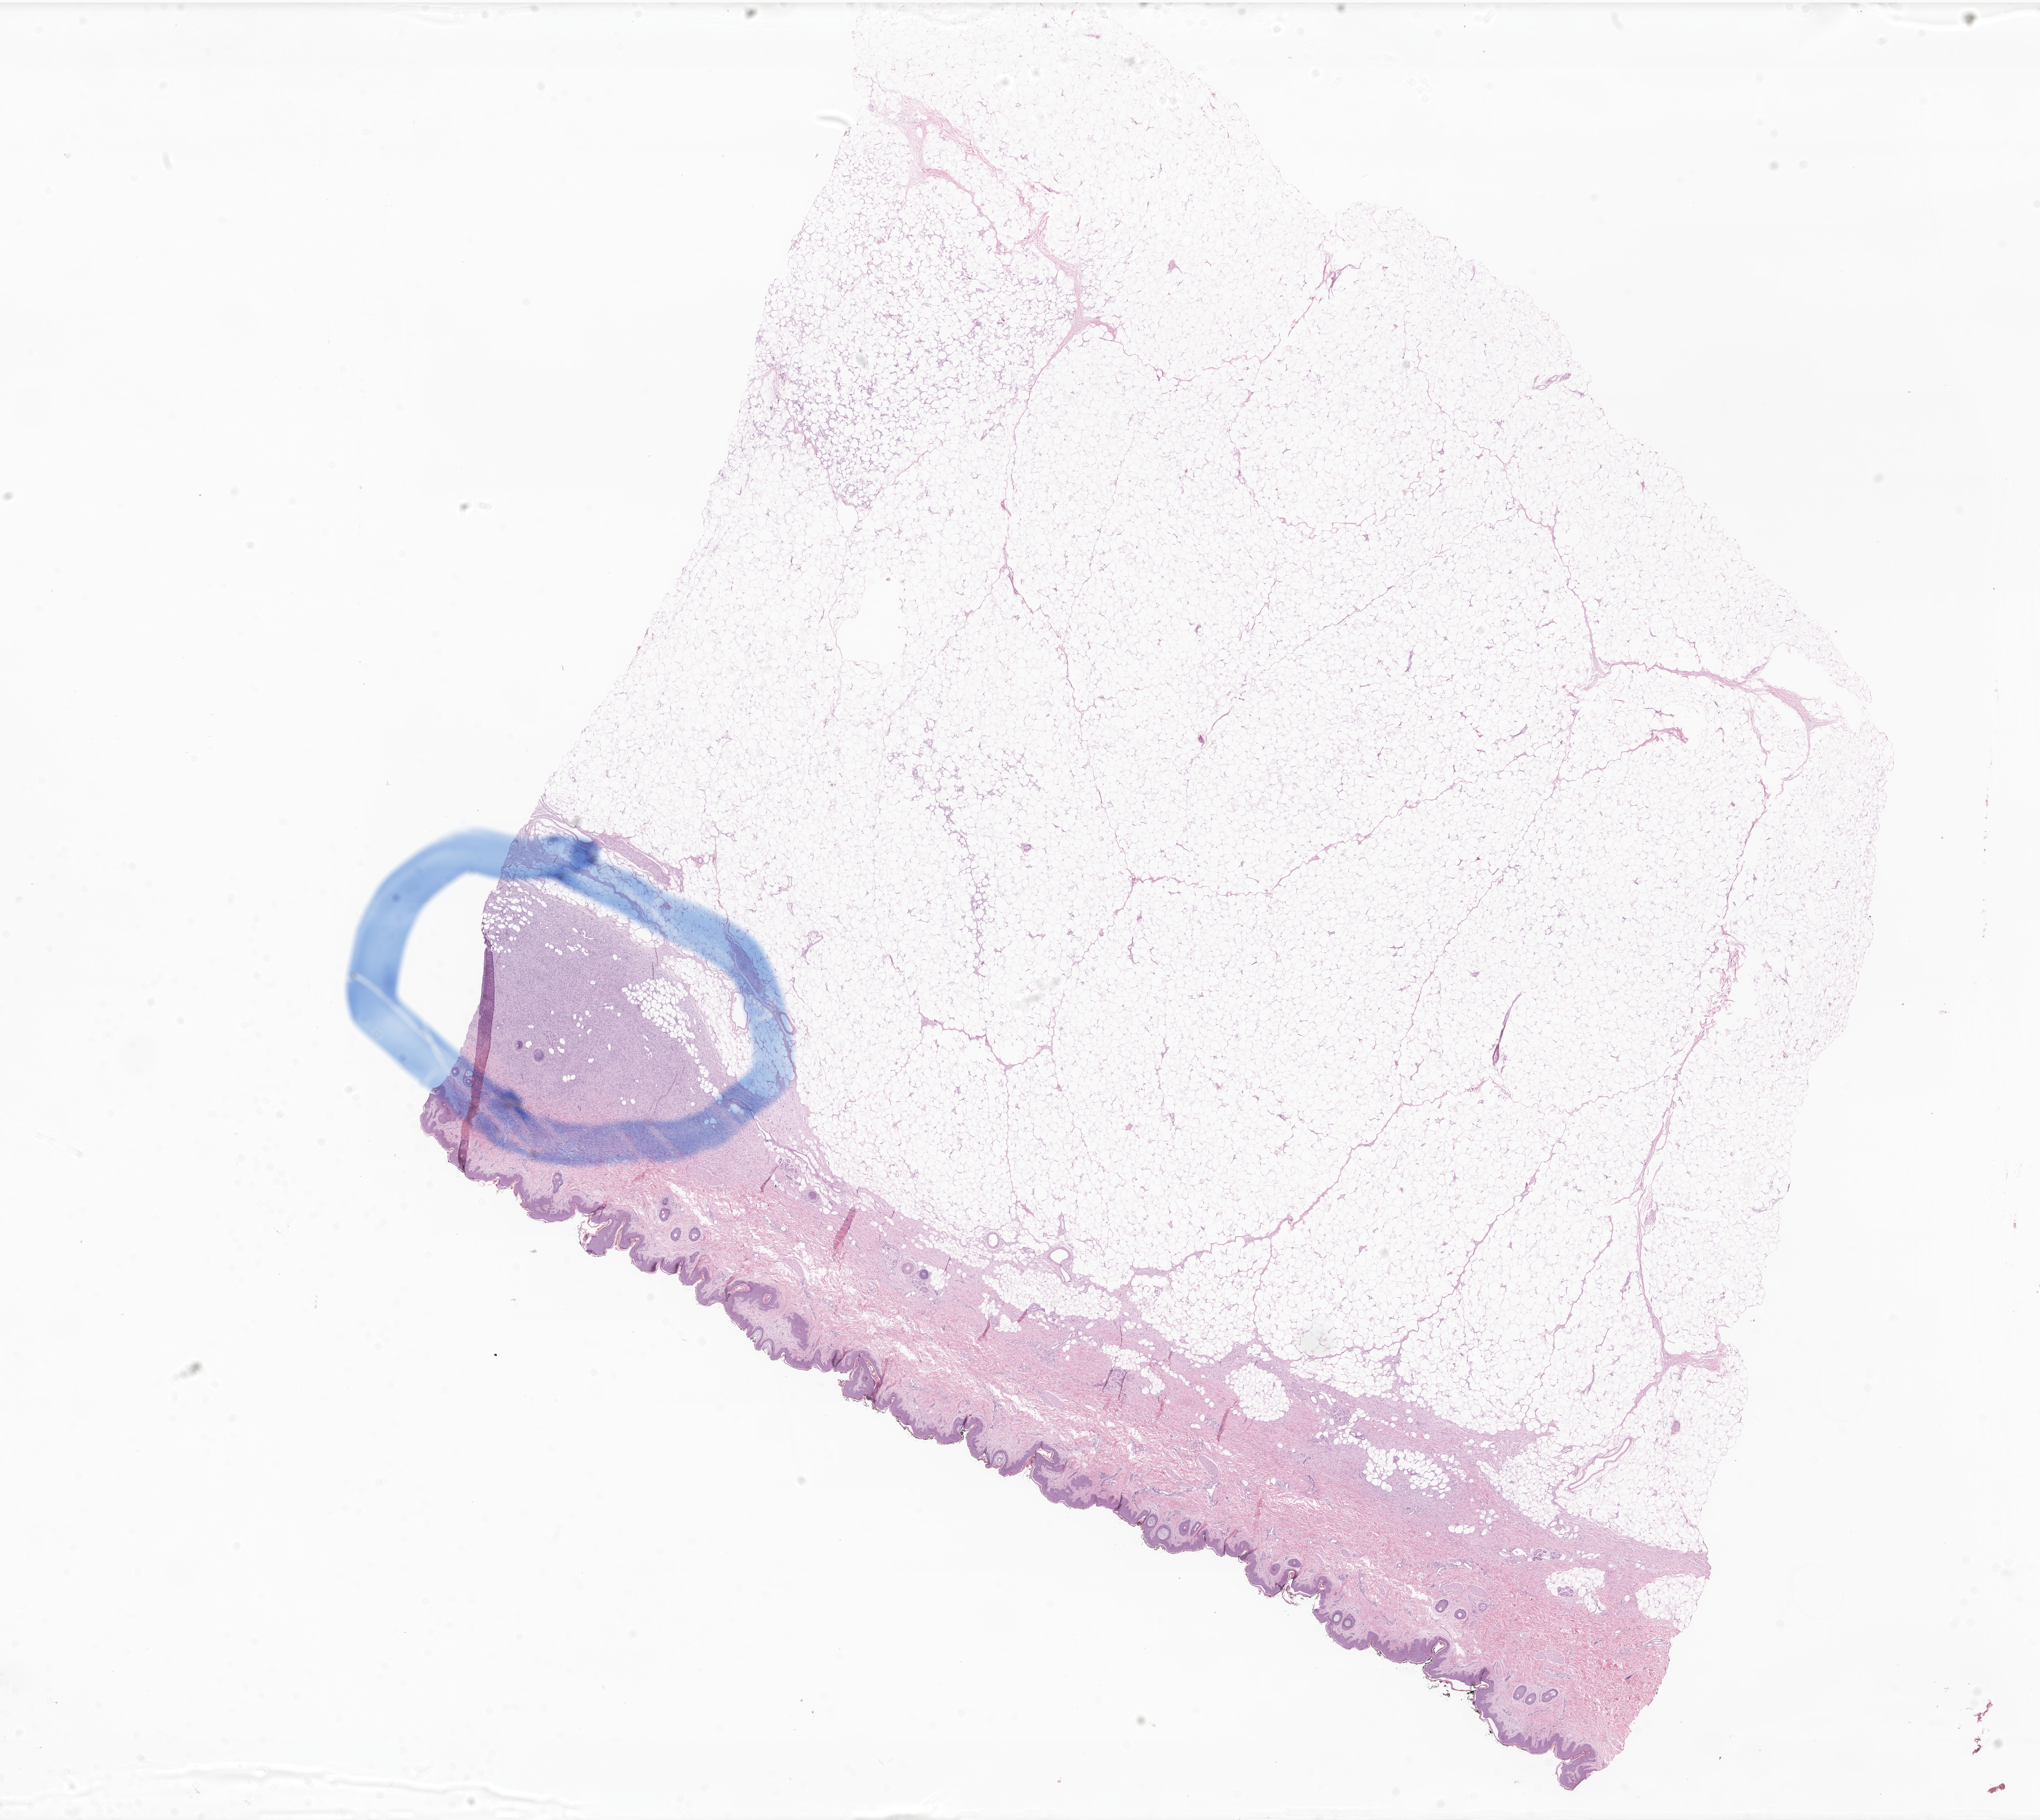
Digitized hematoxylin and eosin (H&E)-stained section of tumor tissue from the soft tissue of pelvis — a low-resolution overview of the entire scanned area, about 26.0 x 23.2 mm; formalin-fixed paraffin-embedded section. Patient female; age 101 months (8 years 5 months).
• tissue or organ of origin (case record): connective, subcutaneous and other soft tissues of pelvis
• diagnosis: Dermatofibrosarcoma protuberans, fibrosarcomatous